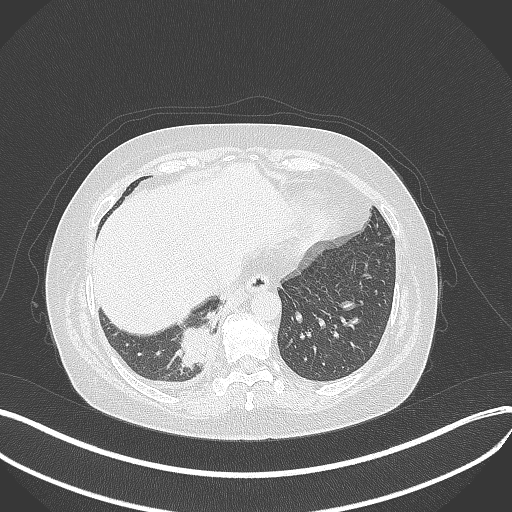
Chest CT, one axial slice; position 93 of 381 along the scan axis; 120 kVp; lung window (W 1500 / L -600 HU); 1 mm slice thickness; 512 × 512 image matrix. Female patient, age 56 years. Case-level facts recorded for this patient, not image findings: clinical TNM (as recorded): T2b N1 M0; histopathological grade: G3.
Annotated regions visible in this slice (rectangle marked by the reading radiologist):
- lung tumour (recorded histology: small cell carcinoma): bounding box (x1, y1, x2, y2) in pixels: (164, 311, 218, 369)